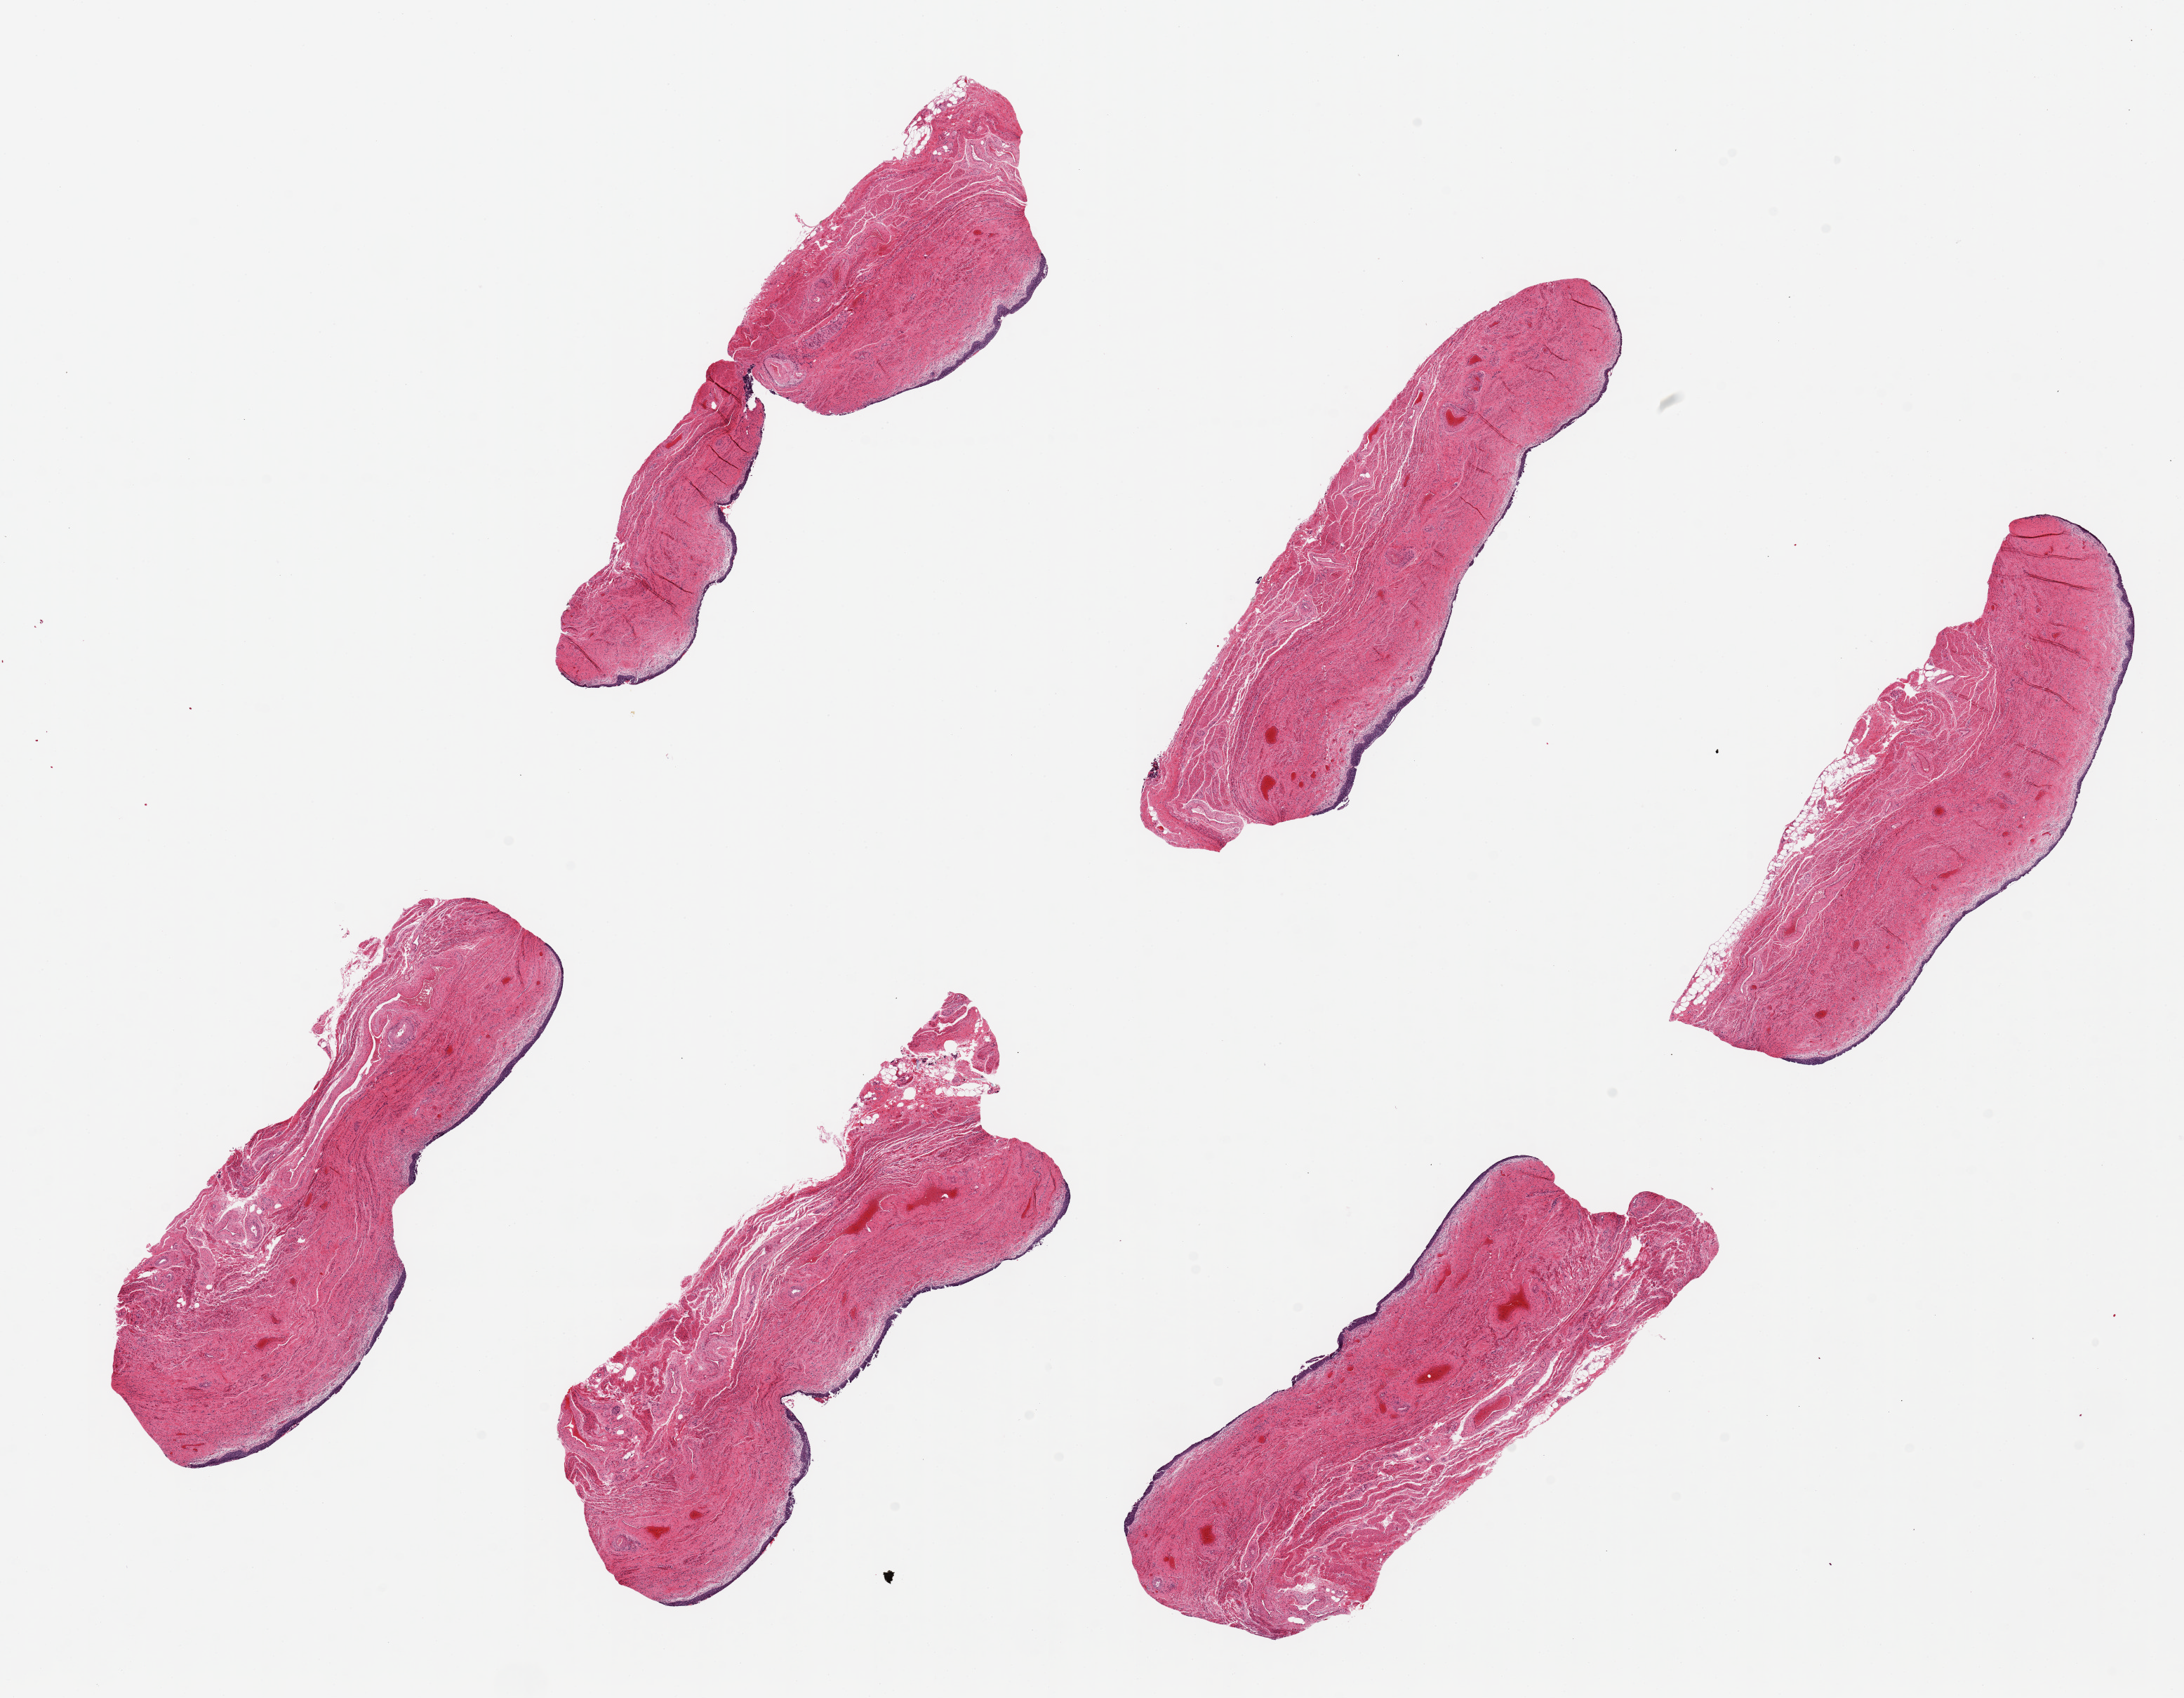
Whole-slide image, H&E stain, brightfield — shown as a low-resolution overview of the whole scanned area (about 24.6 x 19.1 mm, slide scanned at 20x). PAXgene-fixed, paraffin-embedded tissue. Target tissue: vagina. Donor tissue sample. Donor: female.
Review note (as recorded): 6 pieces, up to 8x3mm; squamous epithelium shows high grade dysplasia overall.